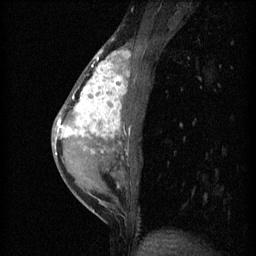
Breast MRI (dynamic contrast-enhanced), one sagittal slice; 3 images stored at this slice position (order not interpretable as contrast timing); 1.5 T; TE 4.2 ms, TR 11 ms; 2 mm slice thickness; 256 × 256 image matrix, field of view 180 × 180 mm. Patient: female, 40 years.
Annotated regions visible in this slice (semi-automatic segmentation, software-assisted and operator-edited):
- analysis volume of interest (the breast-tissue region the enhancement analysis was run in; not a lesion): bounding box (x1, y1, x2, y2) in pixels: (55, 42, 143, 203)
- tumour enhancement mask (voxels above the 70 % enhancement threshold inside the analysis volume of interest): (56, 50, 132, 155)